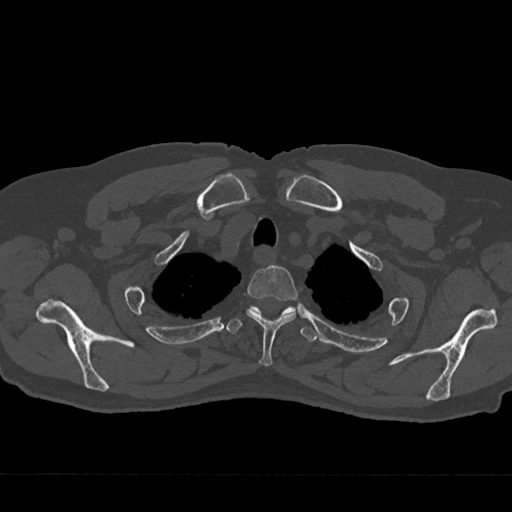
CT including the spine, one axial slice. Slice 599 of 797 in the series (ordered by position). Reconstruction kernel Br40s/3. 120 kVp. Bone window (W 1800 / L 400 HU). 0.5 mm slice thickness. 512 × 512 image matrix, field of view 377 × 377 mm. Patient: male, 75 years. From the clinical record (not read from this slice): primary cancer: renal.
Annotated regions visible in this slice (semi-automatically segmented with operator editing):
- T2 vertebra: bounding box (x1, y1, x2, y2) in pixels: (246, 265, 298, 366)
- T3 vertebra: (226, 306, 317, 342)